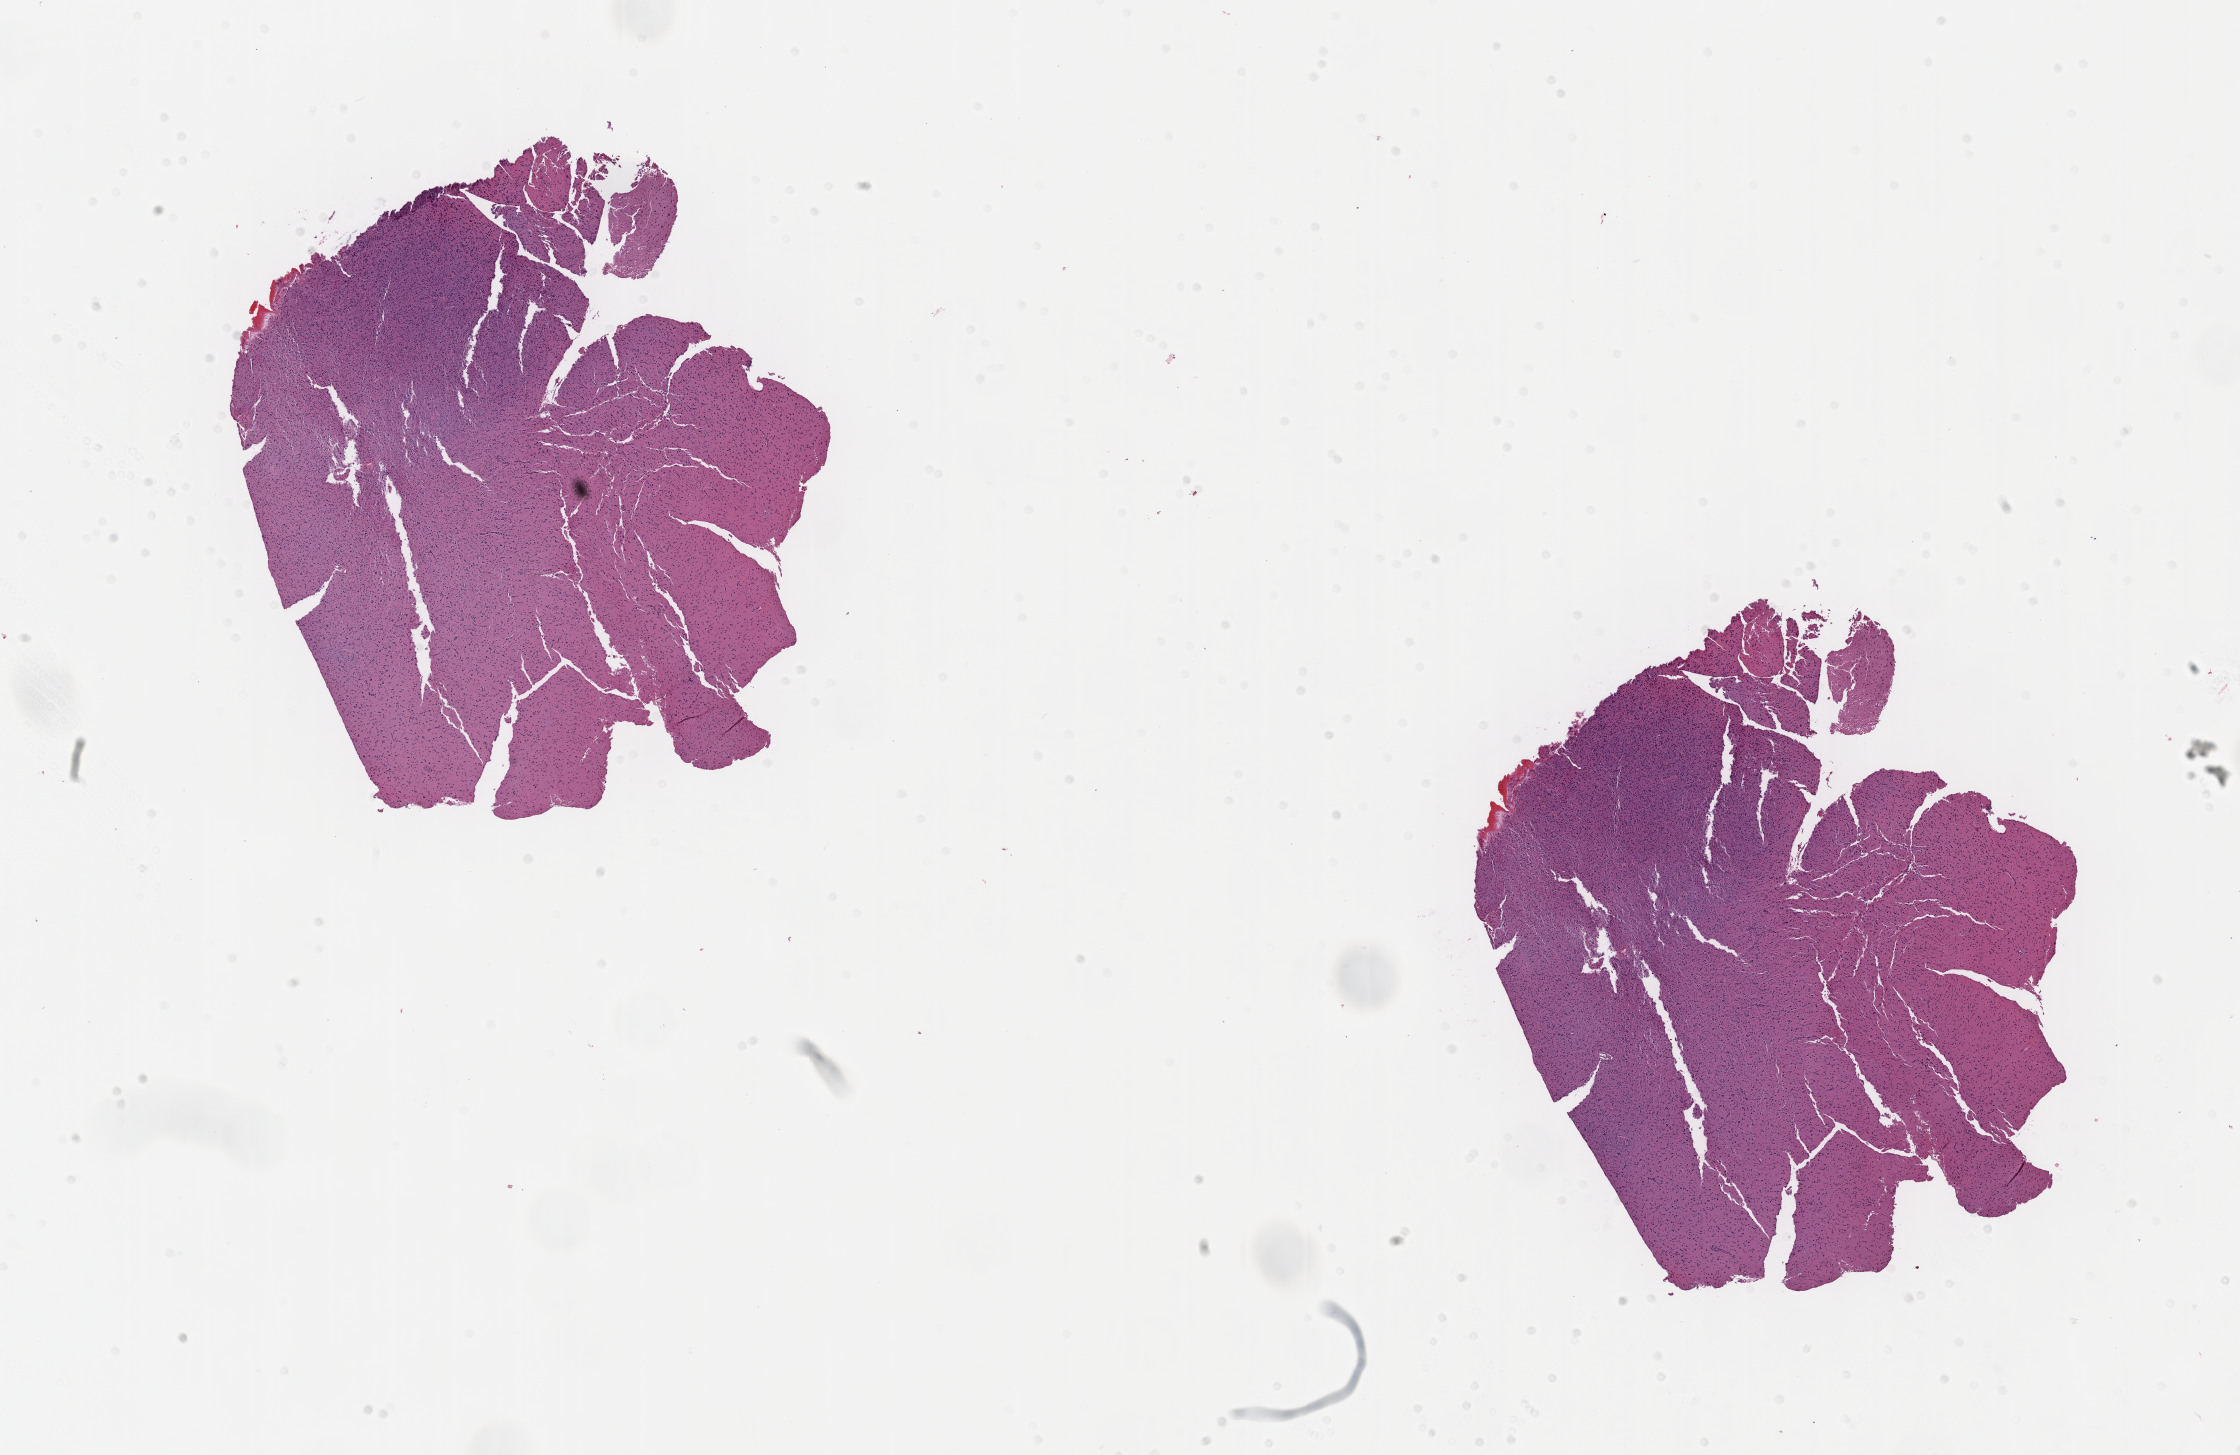
H&E whole-slide image, shown as a low-resolution overview of the whole scanned area (about 18.1 x 11.8 mm). Formalin-fixed paraffin-embedded (FFPE) diagnostic section. Sample: primary tumour, brain. Female, age 58 years at initial diagnosis. Histologic grade: G2 (moderately differentiated).
* laterality: left
* diagnosis: Oligodendroglioma, NOS